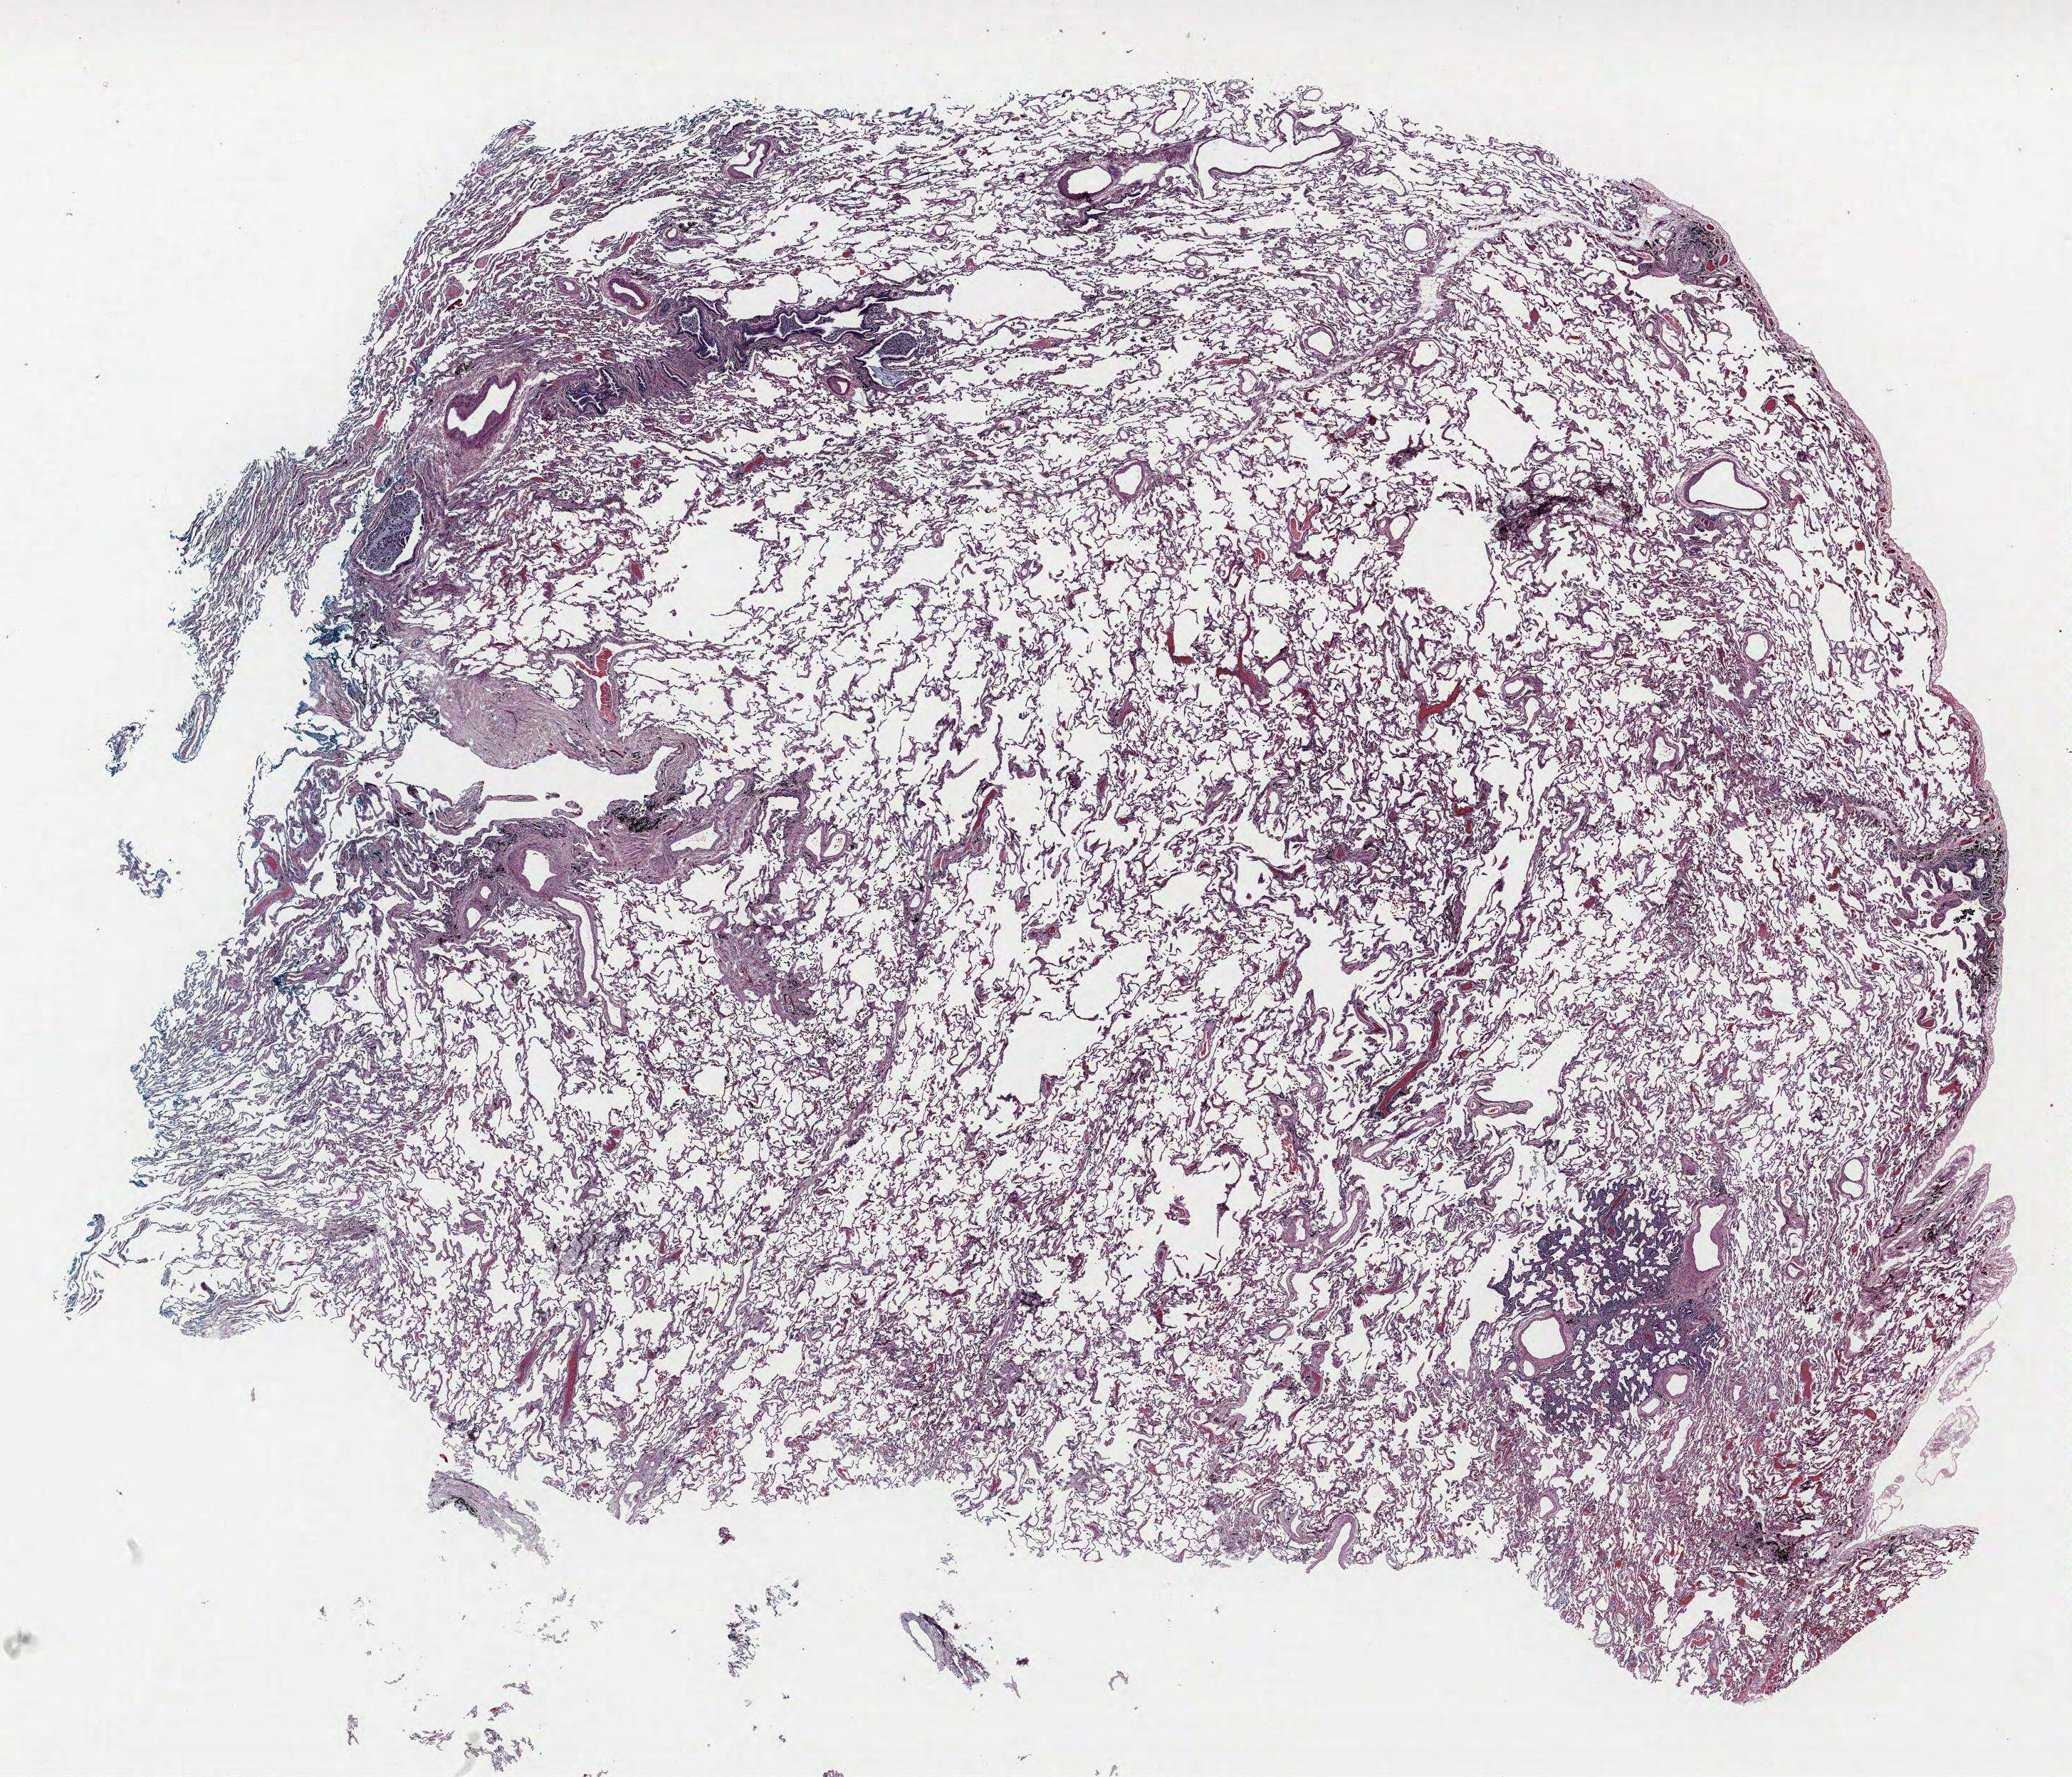
H&E whole-slide image — shown as a low-resolution overview of the whole scanned area (about 23.3 x 20.0 mm, acquisition: 40x scan), FFPE section, lung. Female, age 59 at enrolment. Current smoker at enrolment. Grade: well differentiated (G1).
* ICD-O-3 topography: upper lobe of lung (C34.1)
* participant's lung-cancer diagnosis: Bronchiolo-alveolar adenocarcinoma, NOS
* tumour size (pathology): 4 mm
* primary tumour location (clinical record): right upper lobe
* stage (AJCC 6th edition): IA